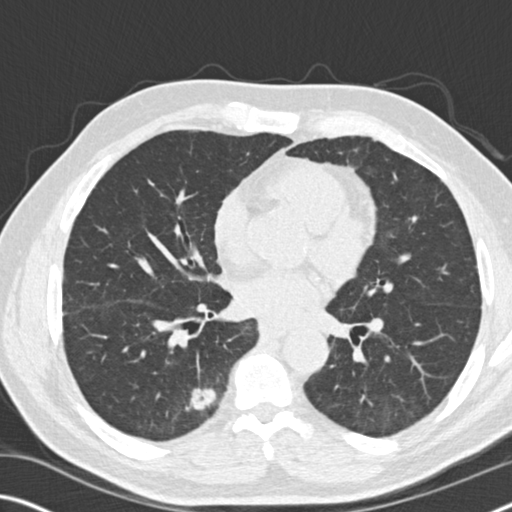
Low-dose screening chest CT, axial slice; baseline screening round; lung window (W 1500 / L -600 HU); standard (soft-tissue) reconstruction kernel (B30f); slice 89 of 169 in the series. Male, age 71 years at enrolment.
Expert-annotated lung lesion, bounding box (x1, y1, x2, y2) in pixels: (159, 373, 229, 433). The screening reader recorded 2 non-calcified nodules or masses ≥4 mm on this exam; which of them this box marks is not recorded.